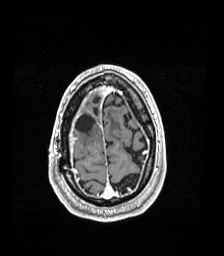
Brain MRI from a brain-tumour surgery series, one axial slice; position 33 of 192 along the scan axis; T1-weighted post-contrast; 1 mm slice thickness; 224 × 256 image matrix, field of view 224 × 256 mm. Case-level facts recorded for this patient, not image findings: histopathology: Astrocytoma; WHO grade: 4; IDH mutation: yes; tumour location: Right Frontal.
Annotated regions visible in this slice (expert manual segmentation):
- previous resection cavity: bounding box [x1, y1, x2, y2] px = [76, 113, 95, 132]
- tumour: [77, 146, 84, 156]